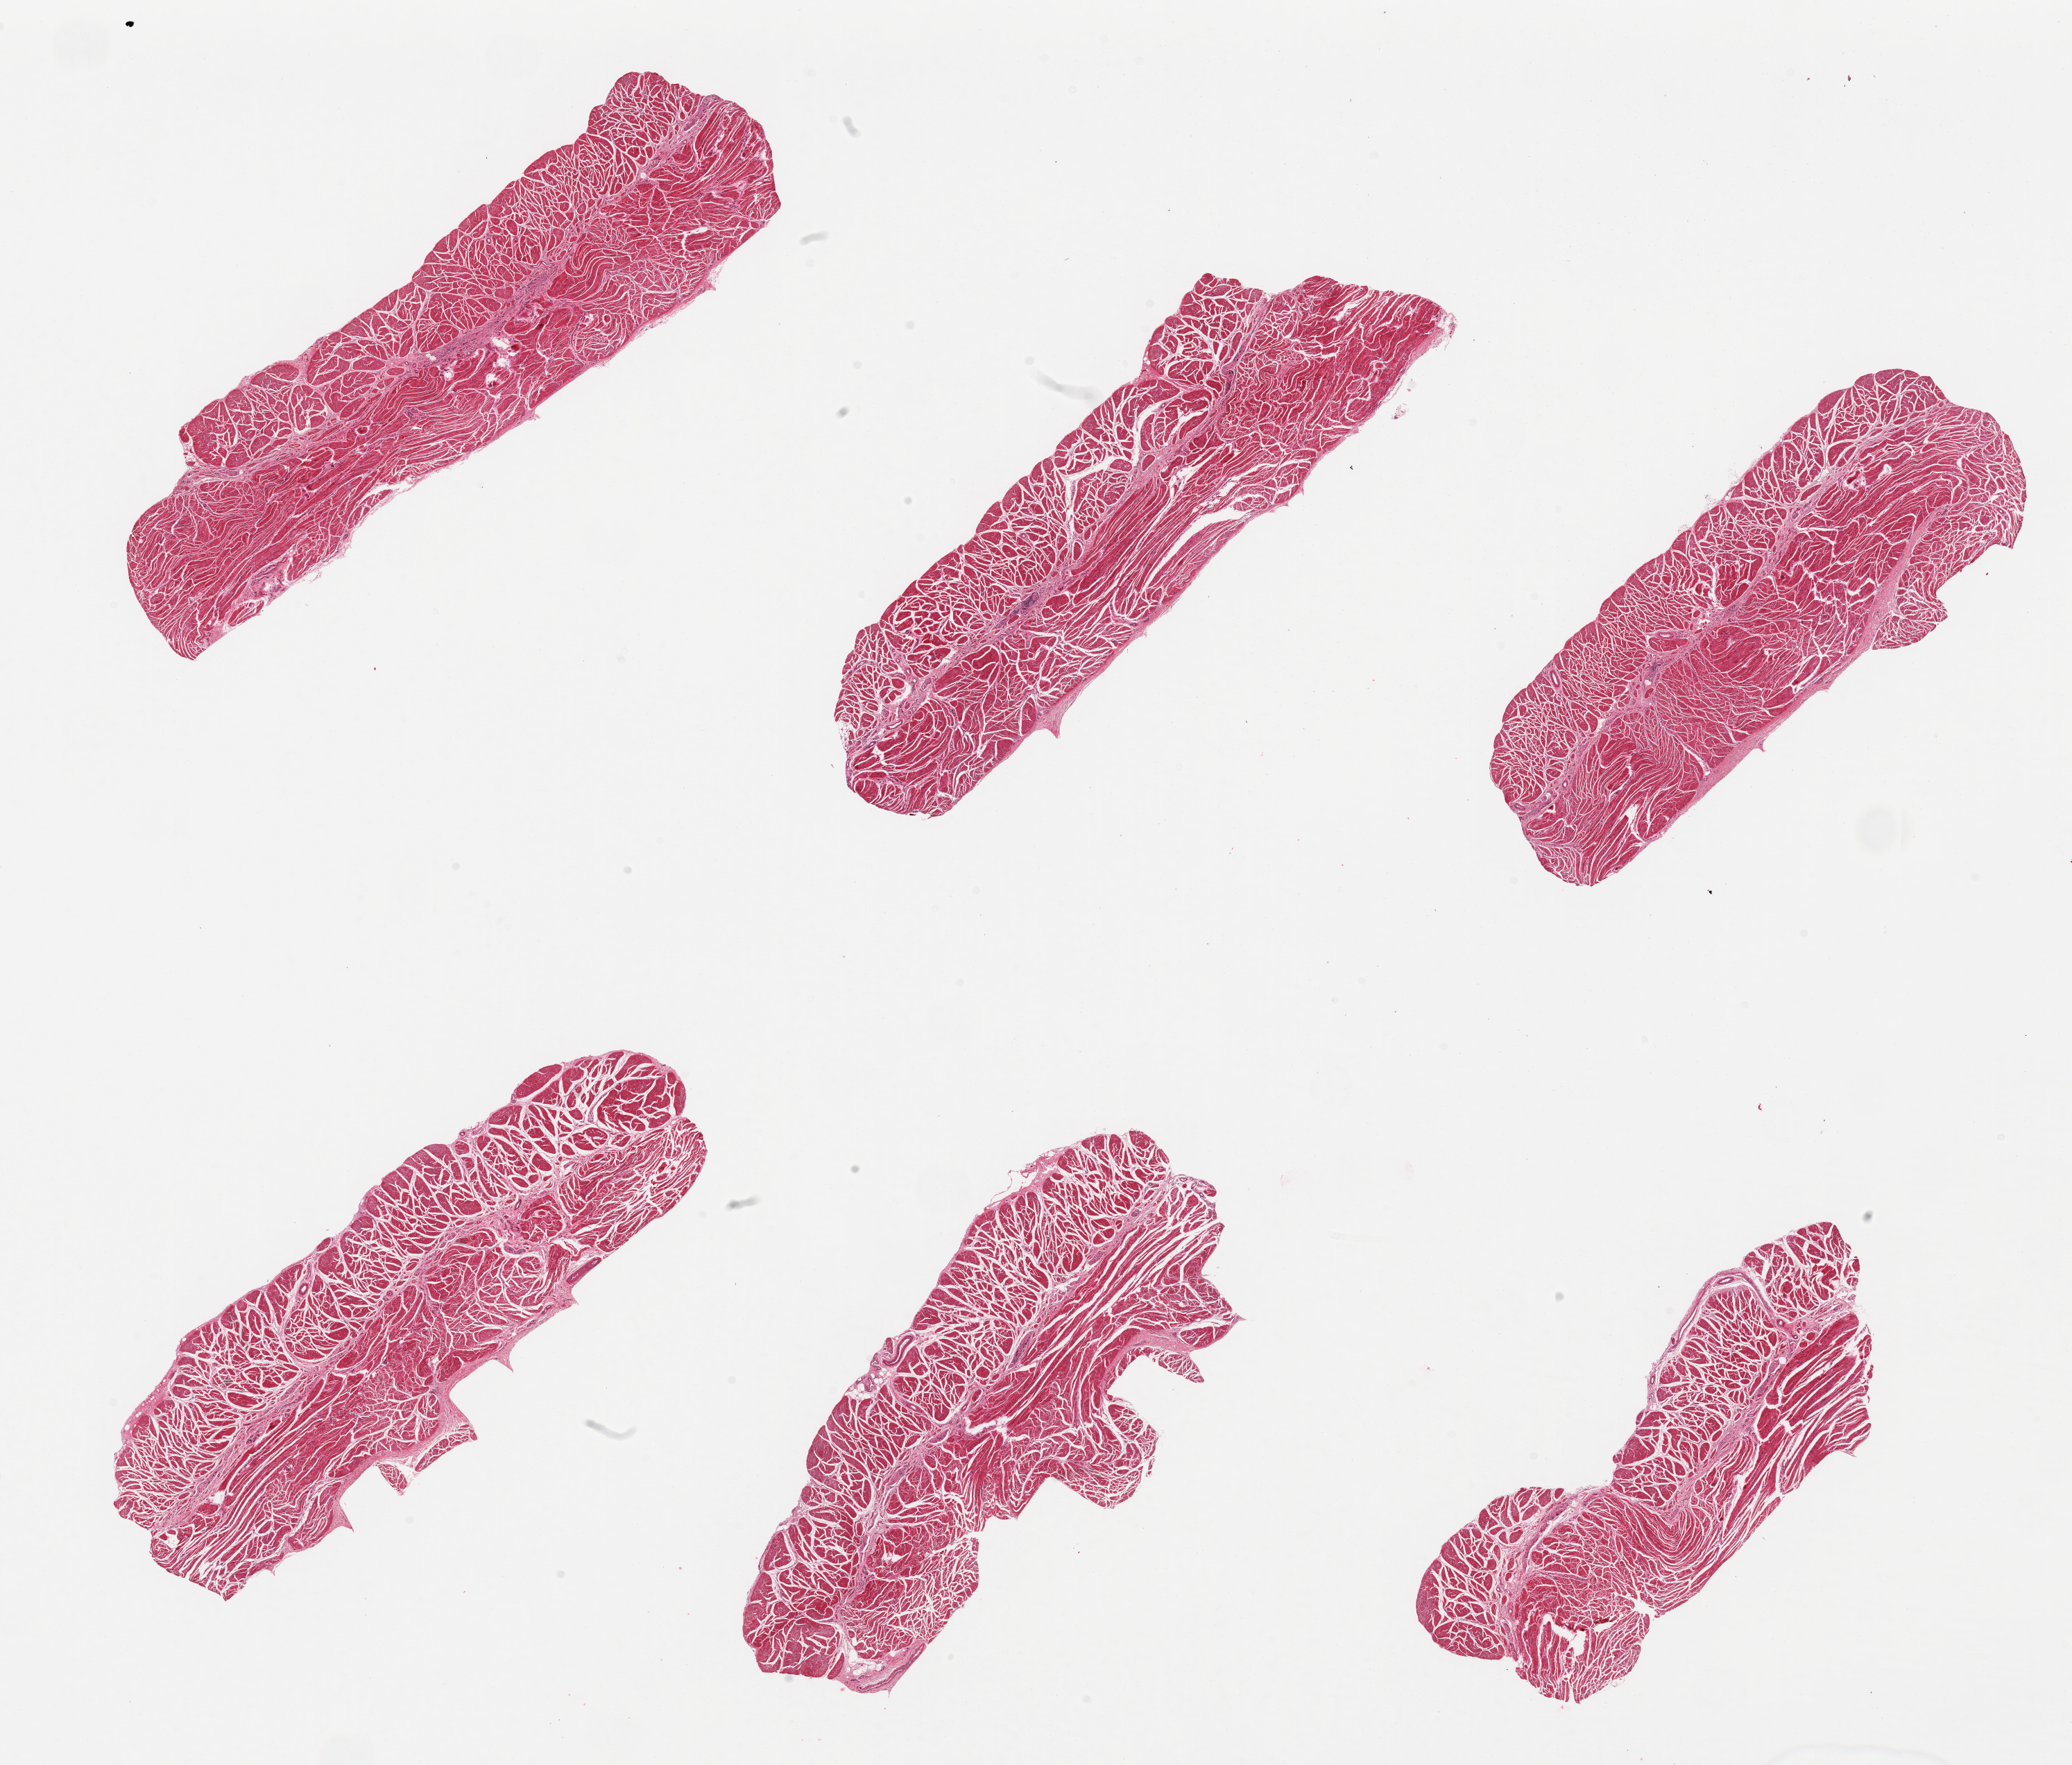
Whole-slide image, H&E stain, brightfield, whole scanned area (about 23.6 x 20.1 mm) shown as a low-resolution overview. PAXgene-fixed paraffin-embedded (PFPE) section. Sampled site (target tissue): esophageal muscle. Tissue donor sample. Donor sex: female.
Pathologist's review note for this sample: 6 pieces; well dissected.